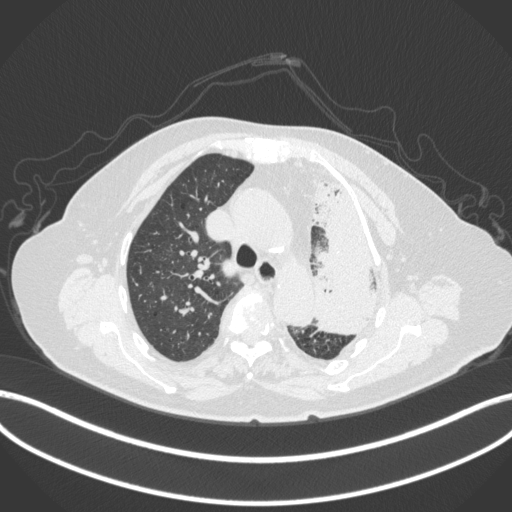
Chest CT, one axial slice. Position 285 of 399 along the scan axis. Reconstruction kernel B31f. Lung window (W 1500 / L -600 HU). 512 × 512 image matrix, field of view 400 × 400 mm. Patient: female, 75 years. Case-level facts recorded for this patient, not image findings: clinical TNM (as recorded): T3 N3 M1.
Outlined on this slice (rectangle marked by the reading radiologist):
- lung tumour (recorded histology: adenocarcinoma): bounding box [x1, y1, x2, y2] px = [307, 174, 391, 340]